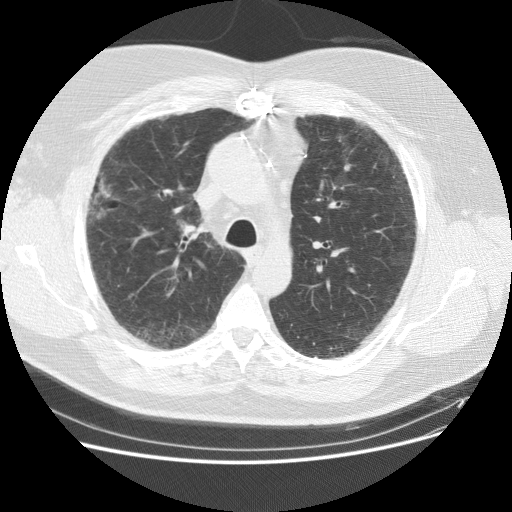
Chest CT (low-dose screening protocol), one axial image, baseline screening round, lung window (W 1500 / L -600 HU), 2.5 mm slice thickness, 120 kVp, slice 41 of 151 in the series, 512 × 512 image matrix, field of view 378 × 378 mm. Male participant, aged 59 years at enrolment. Current smoker at enrolment.
- Lesion marked by an expert reader, bounding box <80,158,128,244> (left, top, right, bottom; pixels).
- The screening reader recorded 2 non-calcified nodules or masses ≥4 mm on this exam (right middle lobe, right lower lobe); which of them this box marks is not recorded.
- Participant outcome: lung cancer diagnosed 338 days after this screen — adenocarcinoma, NOS, right upper lobe, right middle lobe, moderately differentiated (G2), stage IA (AJCC 6th edition), 13 mm at pathology.